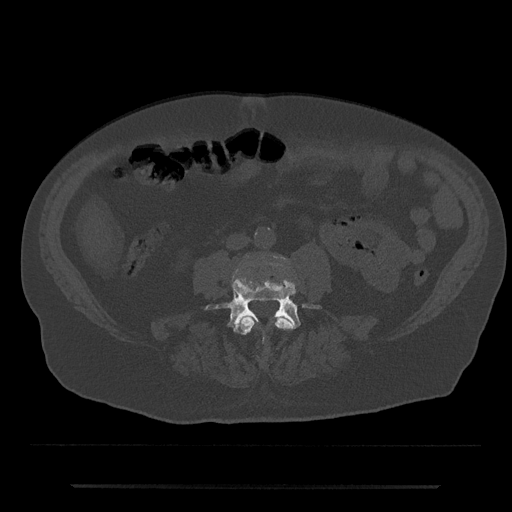
CT including the spine, one axial slice; slice 368 of 797 in the series (ordered by position); reconstruction kernel Br40s/3; bone window (W 1800 / L 400 HU); 0.5 mm slice thickness; 512 × 512 image matrix, field of view 434 × 434 mm. Male patient, age 80 years. Case-level facts recorded for this patient, not image findings: primary cancer: prostate; vertebrae with lytic lesions (as recorded): L1, T11.
Annotated regions visible in this slice (semi-automatically segmented with operator editing):
- L3 vertebra: bounding box <236,316,294,335> (left, top, right, bottom; pixels)
- L4 vertebra: <205,279,321,331>